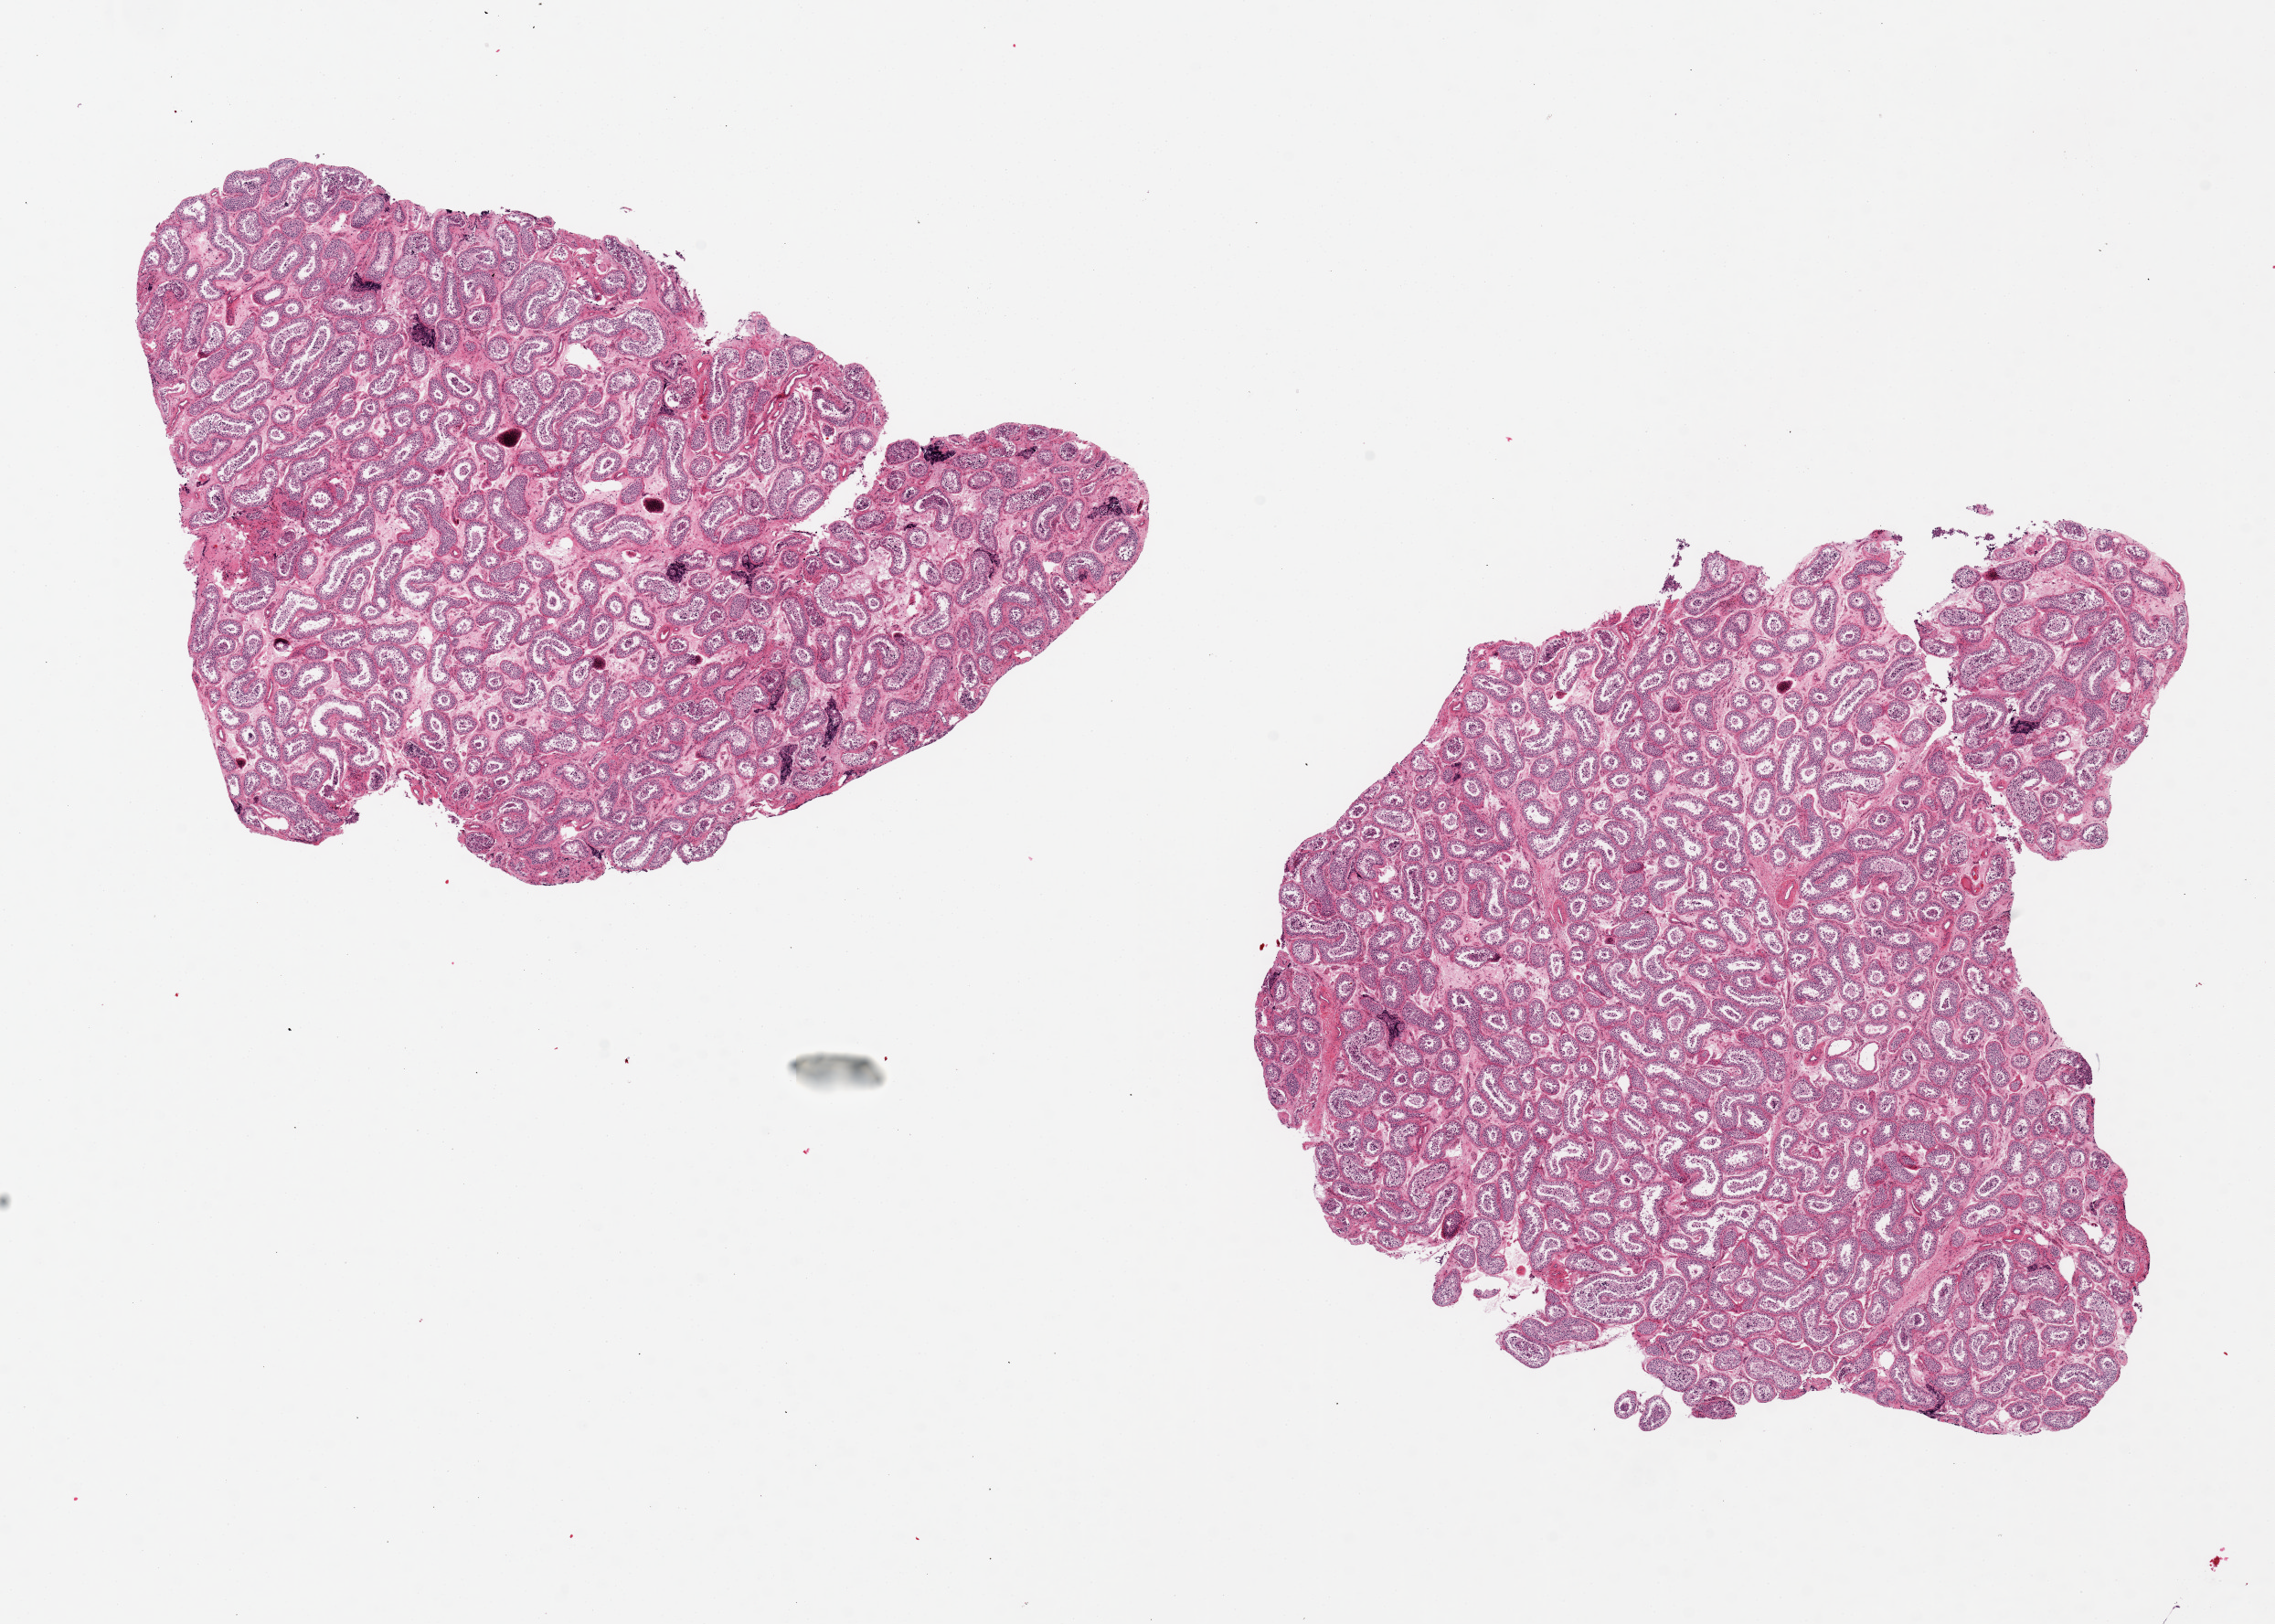
Haematoxylin and eosin whole-slide image, brightfield, shown as a low-resolution overview of the whole scanned area (about 19.7 x 14.1 mm, from a 20x scan), PAXgene-fixed, paraffin-embedded tissue, section of testis (target tissue), tissue donor sample. Donor: male.
* pathologist's review note for this sample: 2 pieces ~8x8mm. Better preserved than usual, spermatogenesis present but appears slightly reduced